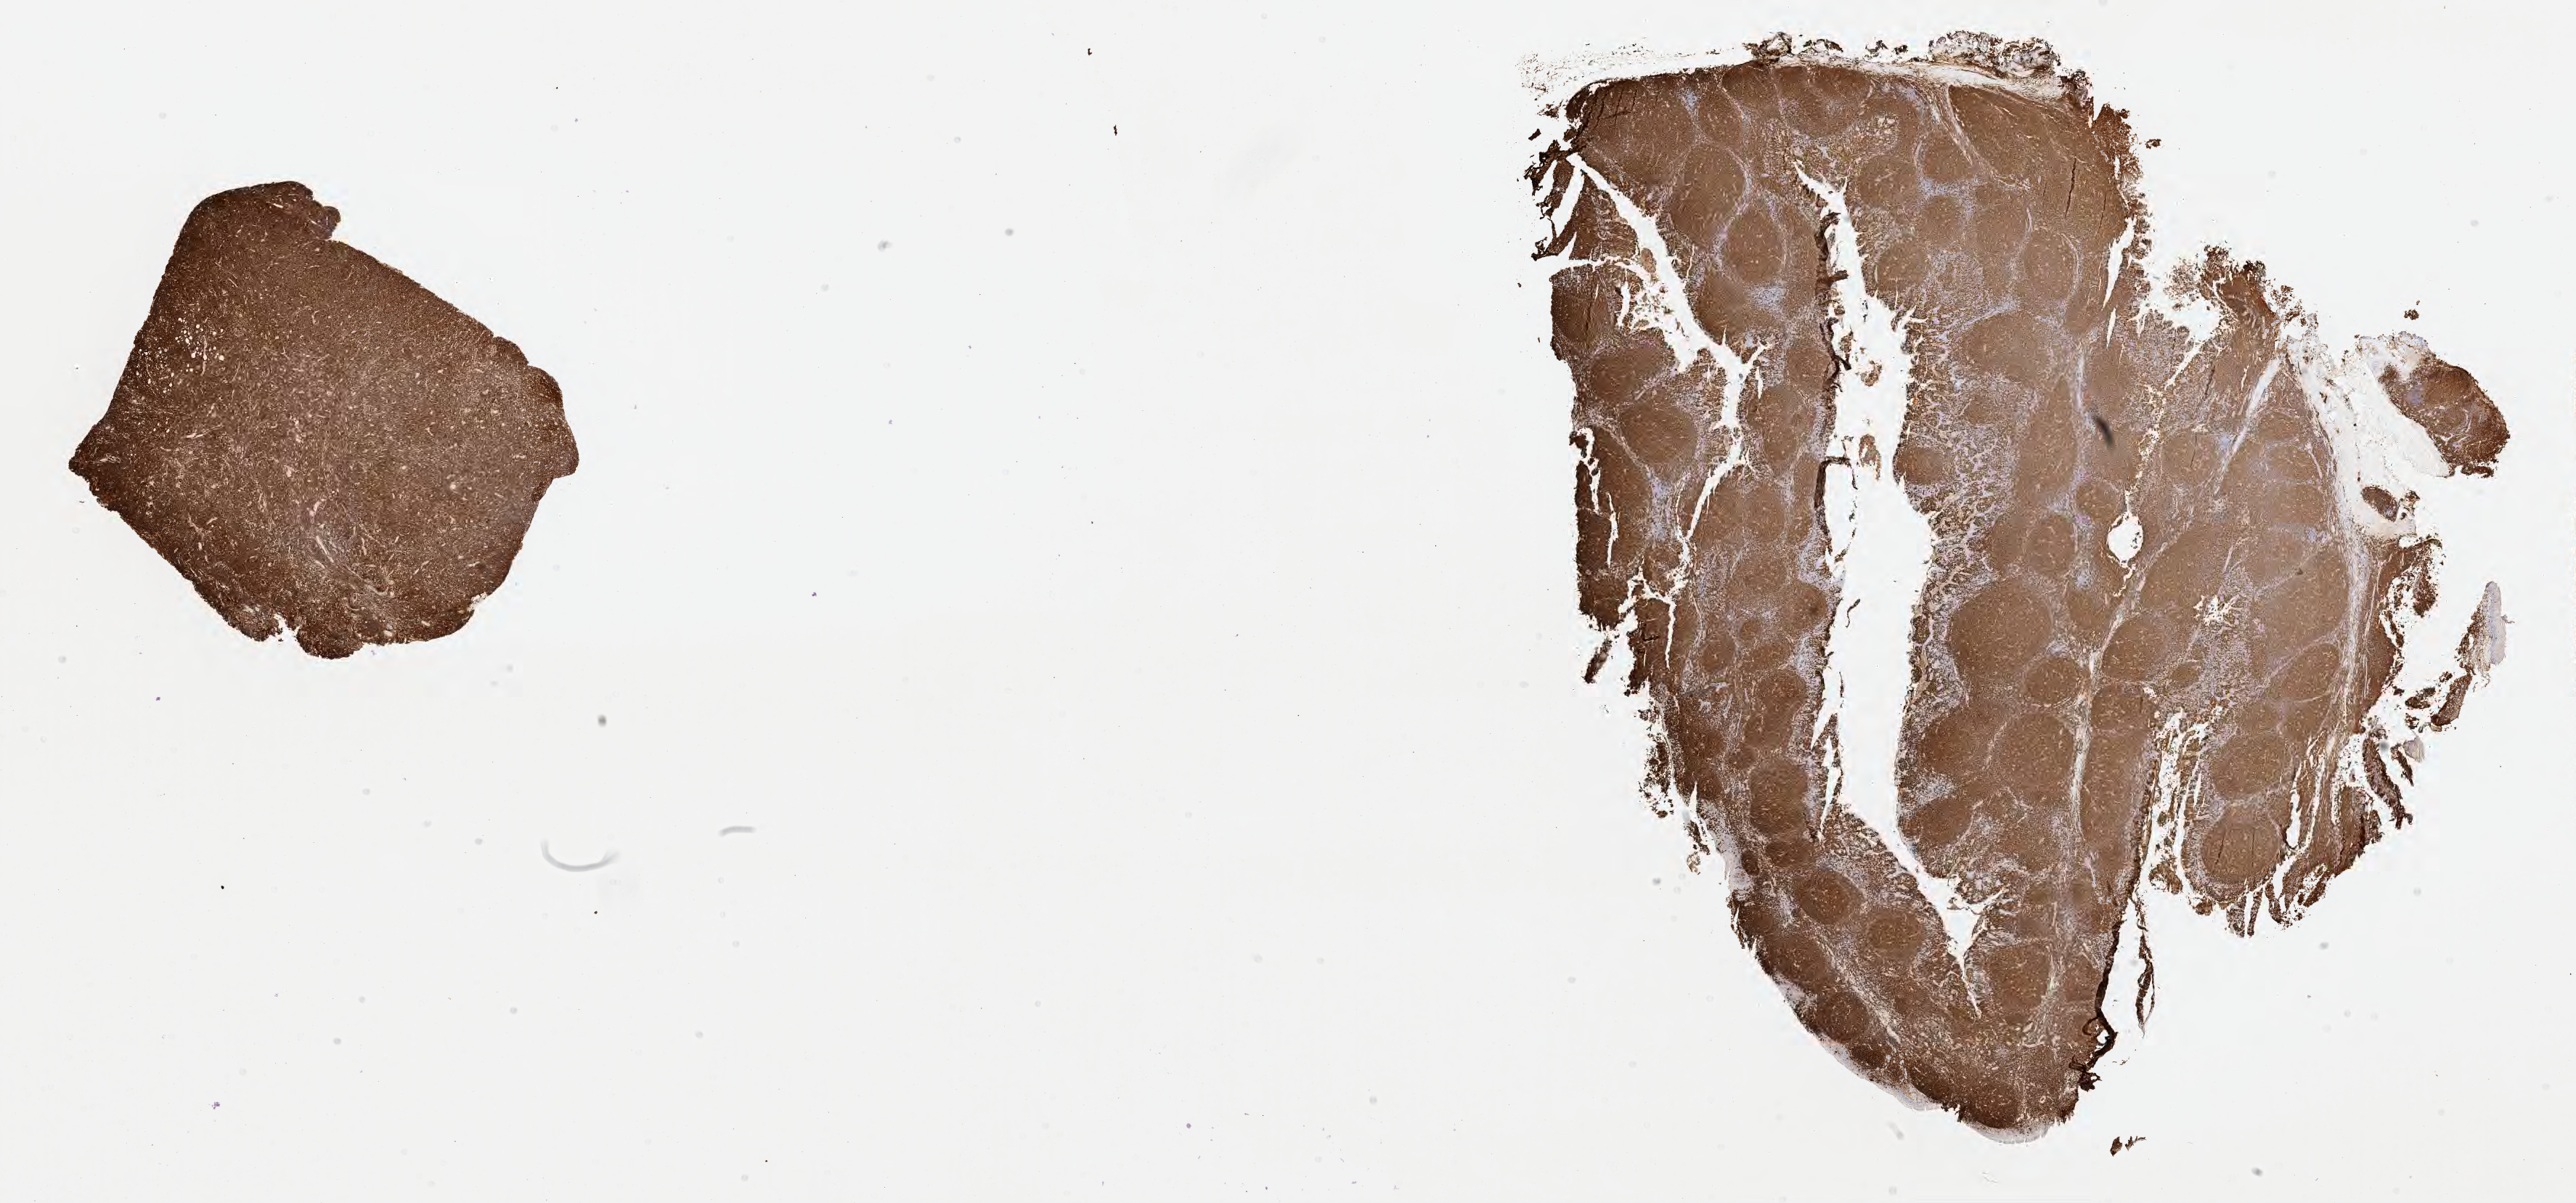
Immunohistochemistry (IHC) whole-slide image stained for CD20 — whole scanned area (about 28.7 x 13.4 mm) shown as a low-resolution overview. Specimen: tumor tissue. Site: buccal mucosa. Male, age 7 years at initial diagnosis.
- diagnosis: Burkitt lymphoma, NOS